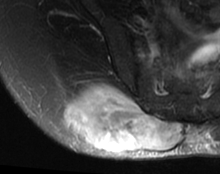
MRI of an extremity soft-tissue mass, one axial slice; T2-weighted fat-saturated; MR volume resampled by the dataset authors to the PET/CT grid (not the native acquisition matrix); 220 × 174 image matrix. Female patient. Case-level facts recorded for this patient, not image findings: histological type: spindle cell suggestive of myxofibrosarcoma; grade: intermediate; site of the primary tumour: right buttock.
Structures marked on this image (expert contour drawn on MRI and transferred to this co-registered scan by the dataset authors):
- gross tumour volume (mass): box from (x=63, y=84) to (x=183, y=153) px